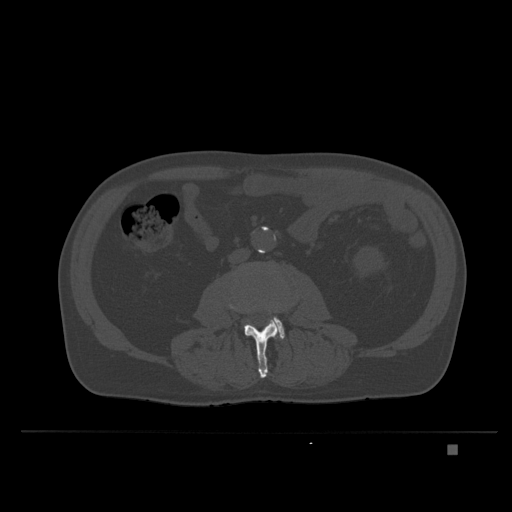
CT including the spine, one axial slice. Slice 90 of 435 in the series (ordered by position). Bone window (W 1800 / L 400 HU). 1.5 mm slice thickness. 512 × 512 image matrix. Male patient, age 73 years. Case-level facts recorded for this patient, not image findings: primary cancer: skin.
Outlined on this slice (semi-automatically segmented with operator editing):
- L3 vertebra: bounding box <229,304,281,378> (left, top, right, bottom; pixels)
- L4 vertebra: <267,317,285,340>